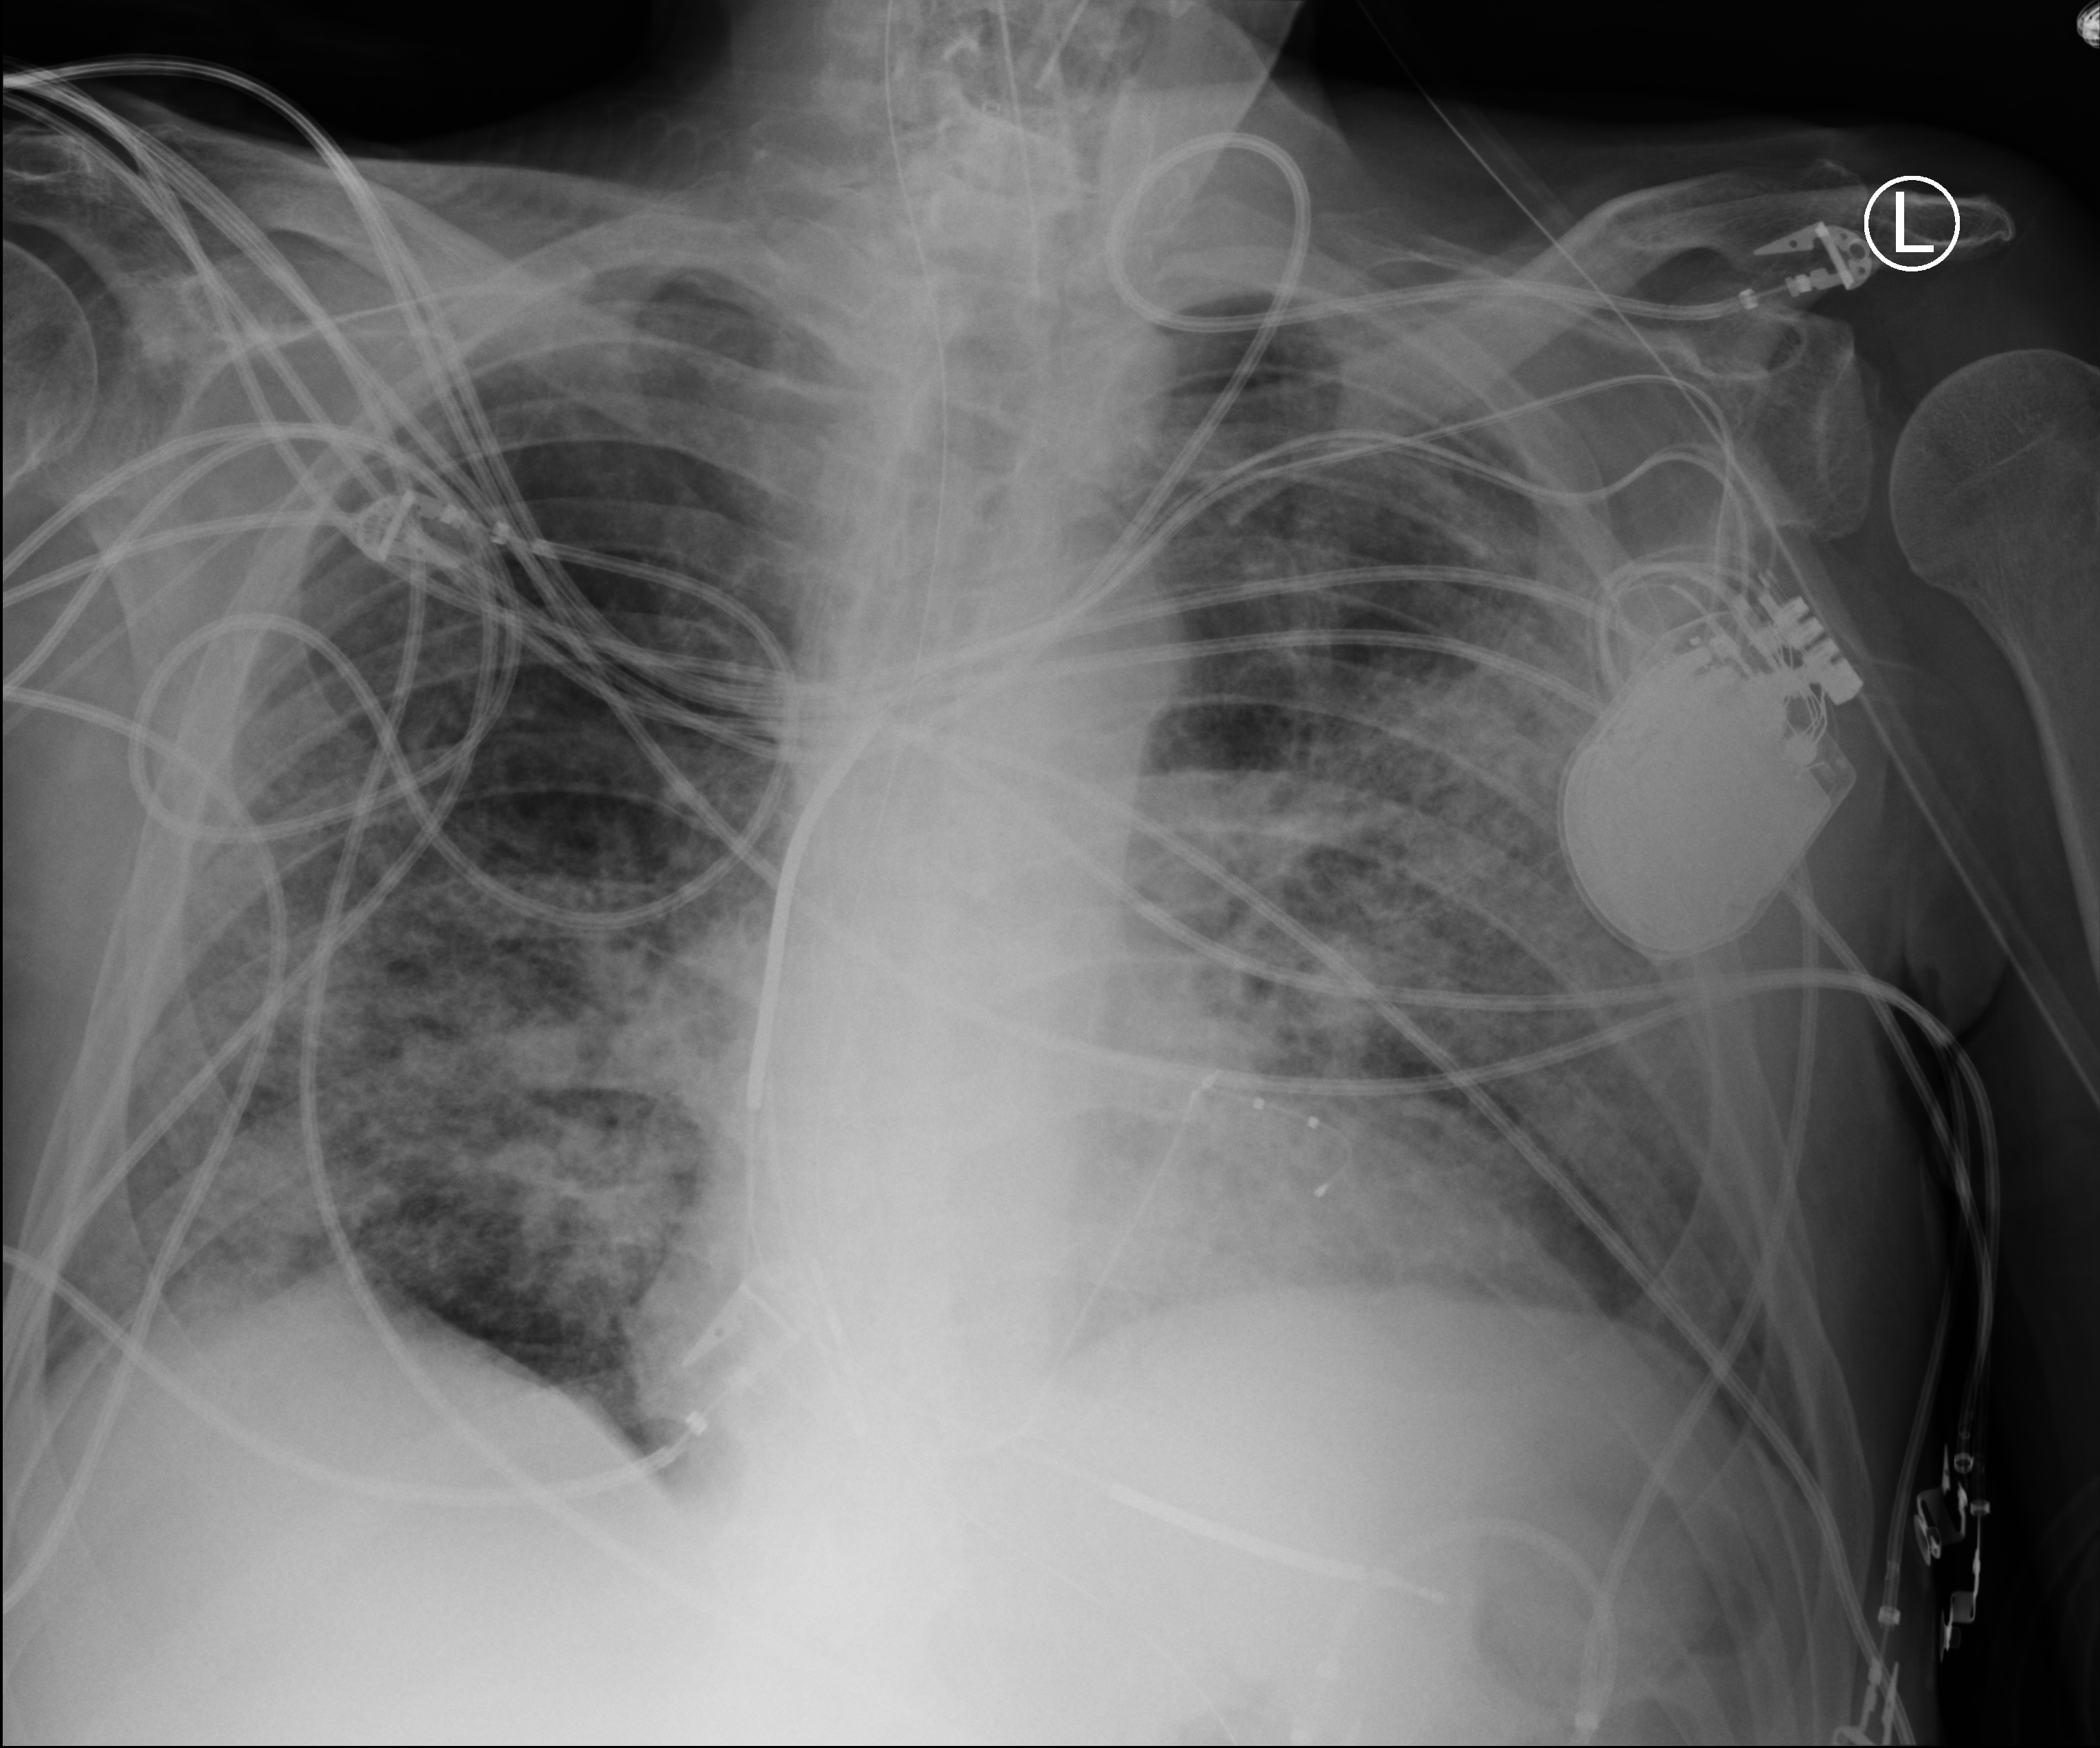
Portable chest radiograph, anteroposterior (AP) projection. Patient hospitalised with COVID-19; male, aged 60–74 years.
Hospital-stay facts (about this admission, not read from this image; timing relative to this image not recorded):
- mechanically ventilated during this hospital stay: yes